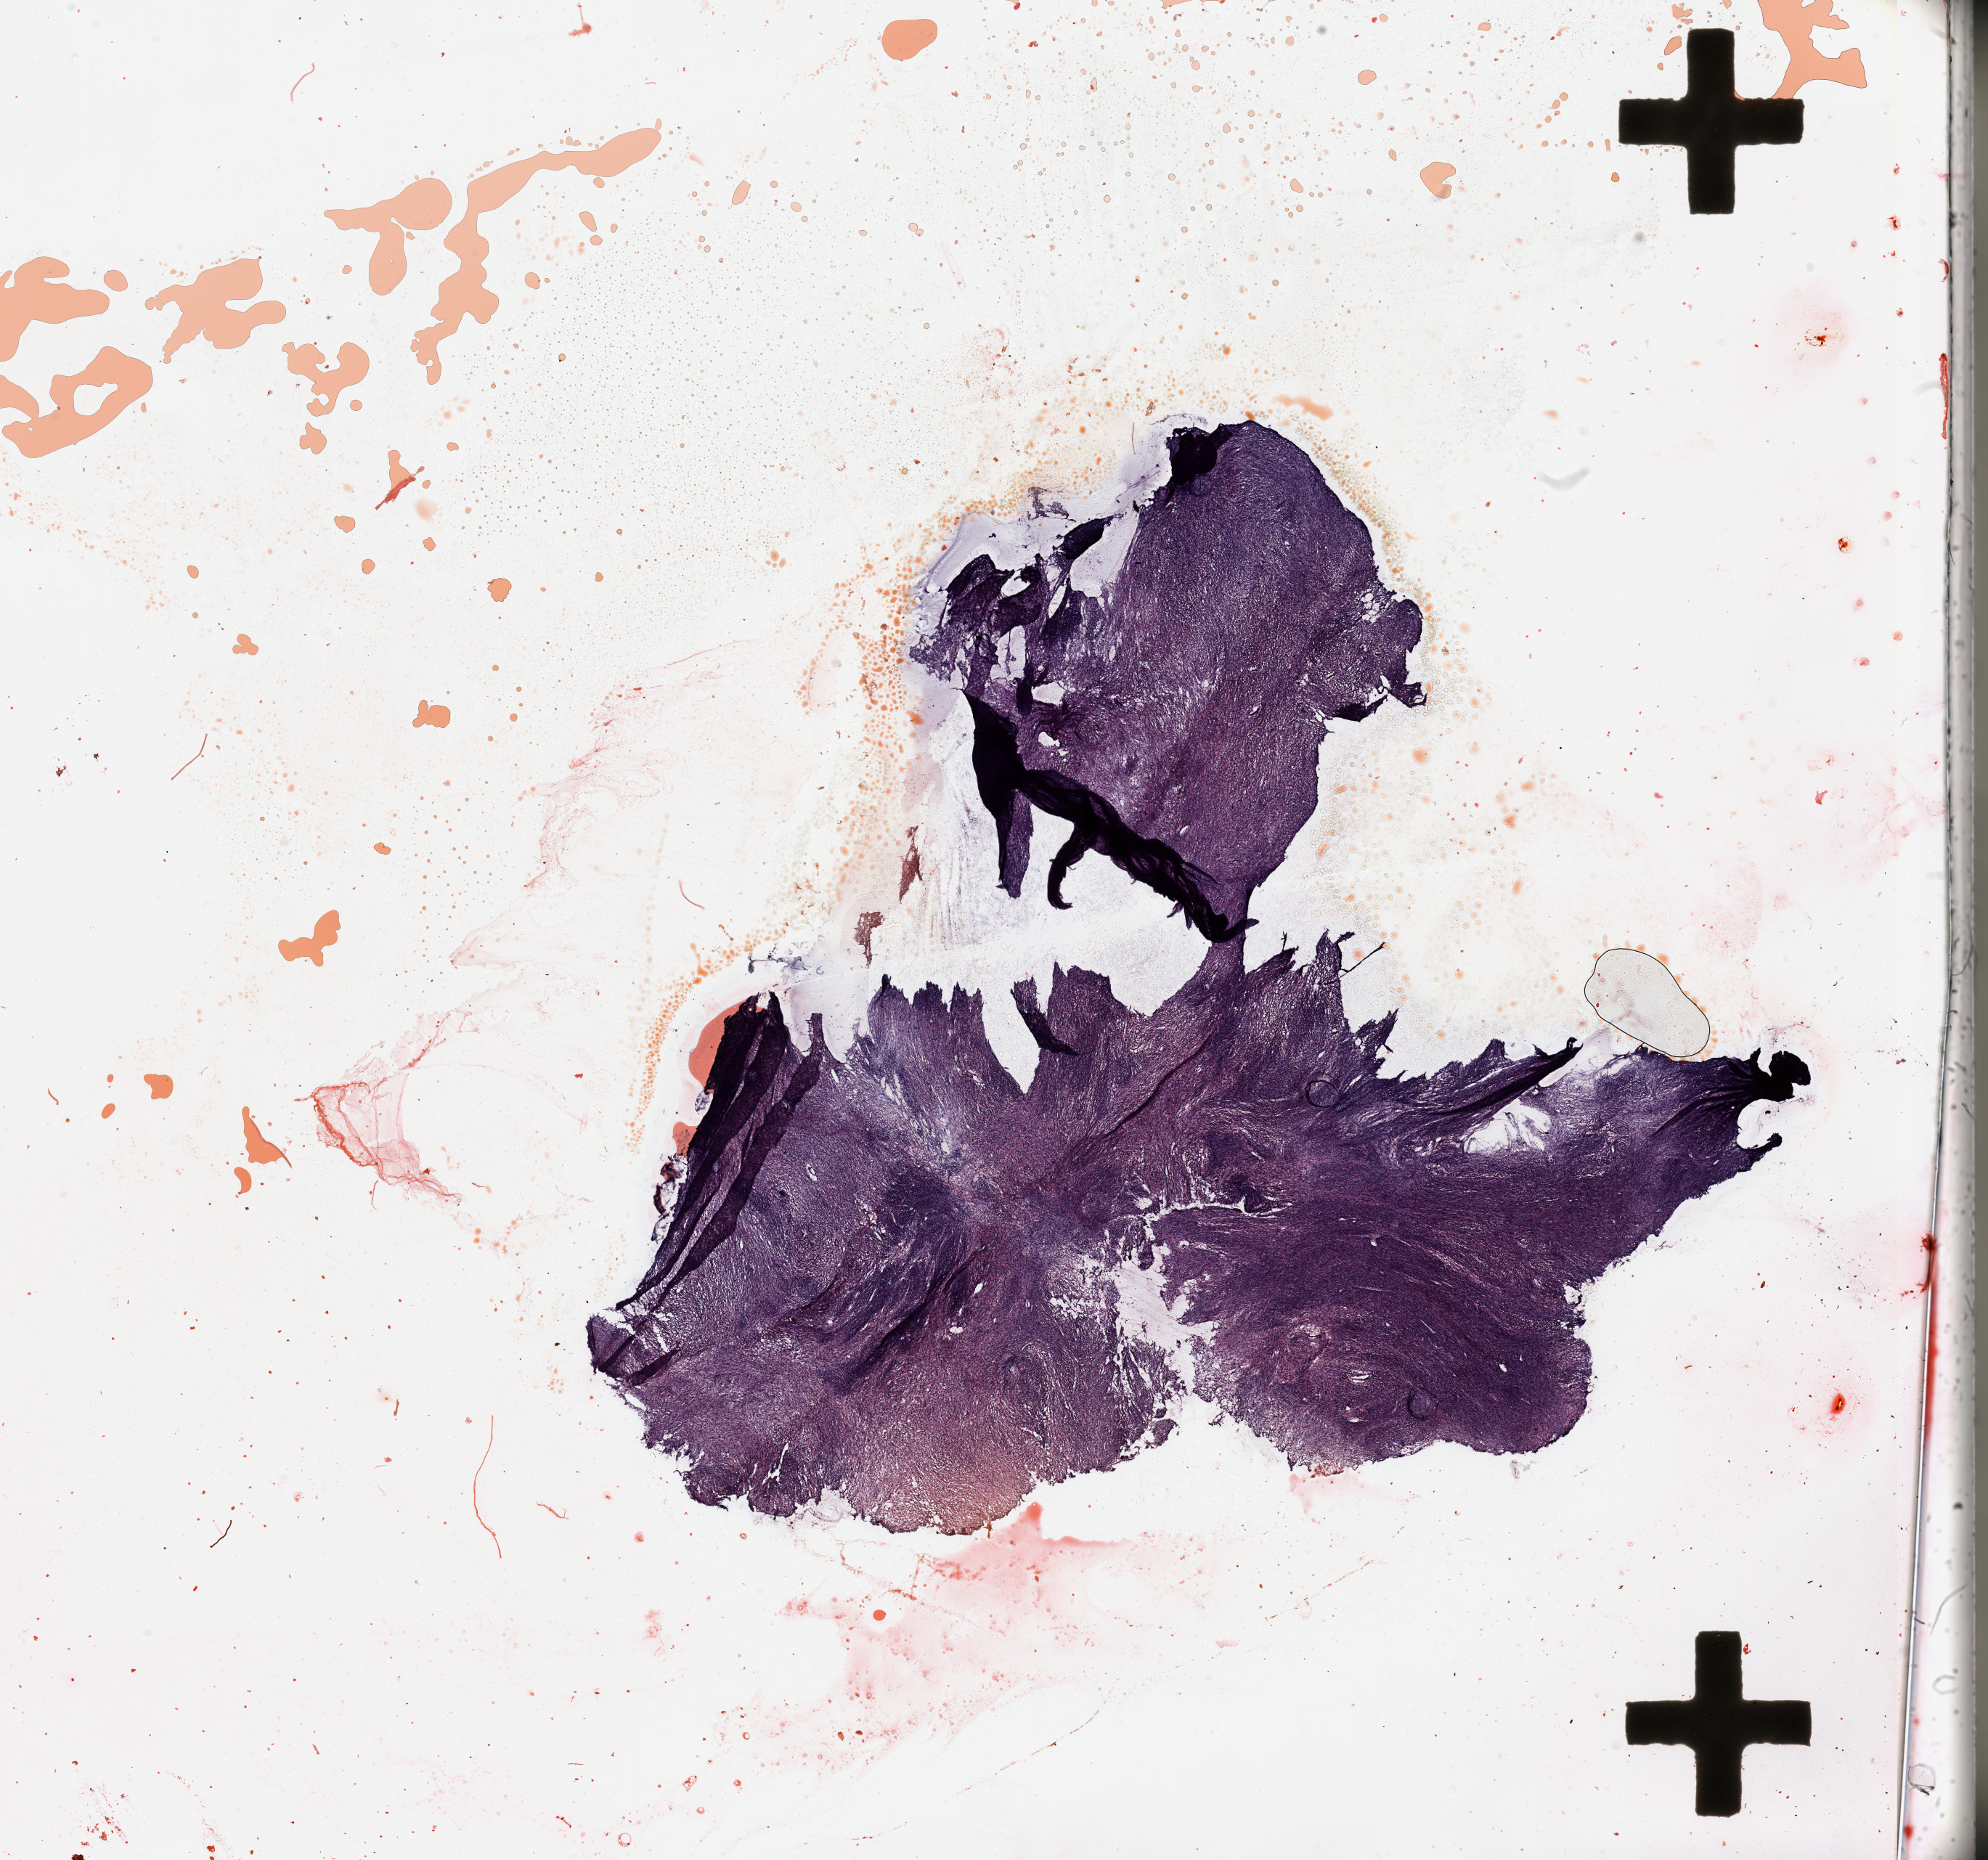
H&E-stained whole-slide image — whole scanned area (about 21.7 x 20.3 mm, from a 20x scan) shown as a low-resolution overview. 65-year-old female patient.
Patient diagnosis (cohort enrolment): sarcoma (site not recorded at cohort level). Primary tumour site (as recorded): gynecologic.